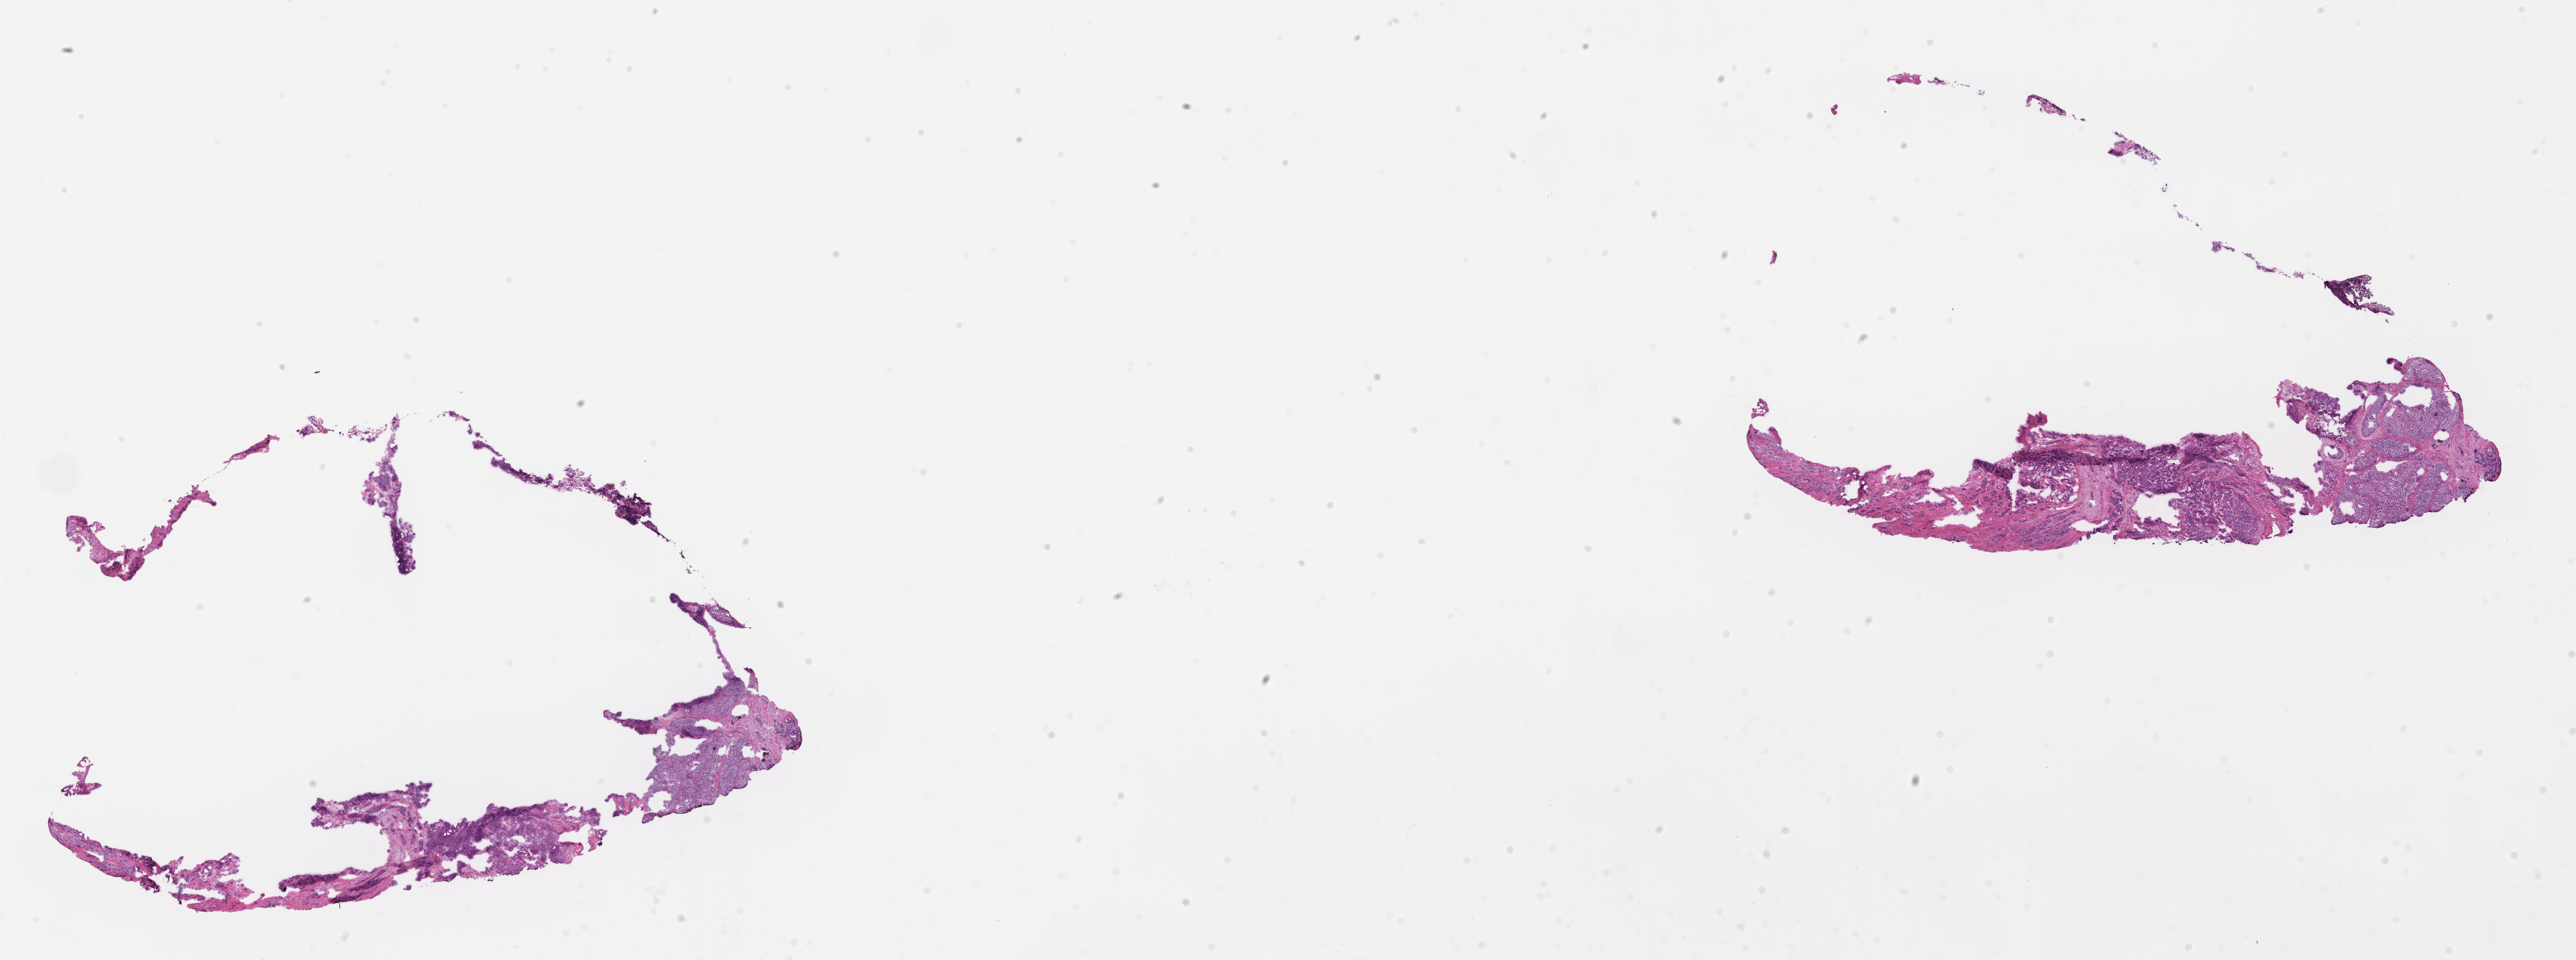
Hematoxylin and eosin (H&E) whole-slide image, low-resolution overview of the scanned area, about 27.6 x 10.3 mm. Cryosection. Primary tumor. Site: breast (right). Patient: female, age at initial diagnosis 55 years. Composition of this section per pathologist review: tumor cells 70%, tumor nuclei 70%, stromal cells 20%, necrosis 0%, normal cells 10%. Infiltration values recorded for this section: lymphocyte infiltration 5%, monocyte infiltration 2%, neutrophil infiltration 0%.
* section: bottom of the tissue portion
* histologic diagnosis: Lobular carcinoma, NOS